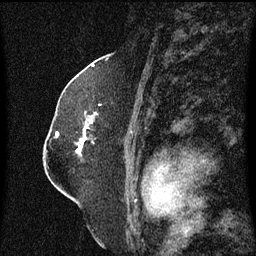
Breast MRI (dynamic contrast-enhanced), one sagittal slice. Position 39 of 60 along the scan axis. Dynamic contrast-enhanced series, image 2 of 3 at this slice position (ordered by acquisition). 1.5 T. TE 4.2 ms, TR 8.4 ms. 2 mm slice thickness. 256 × 256 image matrix, field of view 200 × 200 mm. Patient: female, 52 years. Case-level facts recorded for this patient, not image findings: setting: breast cancer imaged before/during neoadjuvant chemotherapy; receptor status: HR-positive, HER2-negative.
Outlined on this slice (semi-automatic segmentation, software-assisted and operator-edited):
- analysis volume of interest (the breast-tissue region the enhancement analysis was run in; not a lesion): bounding box (x1, y1, x2, y2) in pixels: (77, 104, 102, 163)
- tumour enhancement mask (voxels above the 70 % enhancement threshold inside the analysis volume of interest): (77, 120, 93, 155)